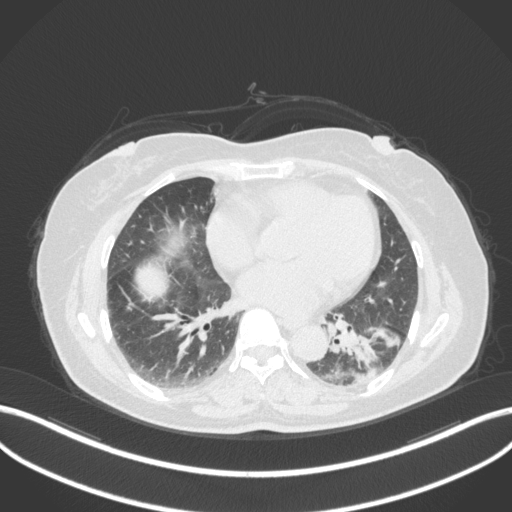
Chest CT, one axial slice. Slice 158 of 307 in the series (ordered by position). Reconstruction kernel B31f. 120 kVp. Lung window (W 1500 / L -600 HU). 512 × 512 image matrix, field of view 400 × 400 mm. Patient: female, 59 years. From the clinical record (not read from this slice): clinical TNM (as recorded): T2a N0 M0.
Outlined on this slice (rectangle marked by the reading radiologist):
- lung tumour (recorded histology: adenocarcinoma): bounding box [x1, y1, x2, y2] px = [323, 325, 405, 384]